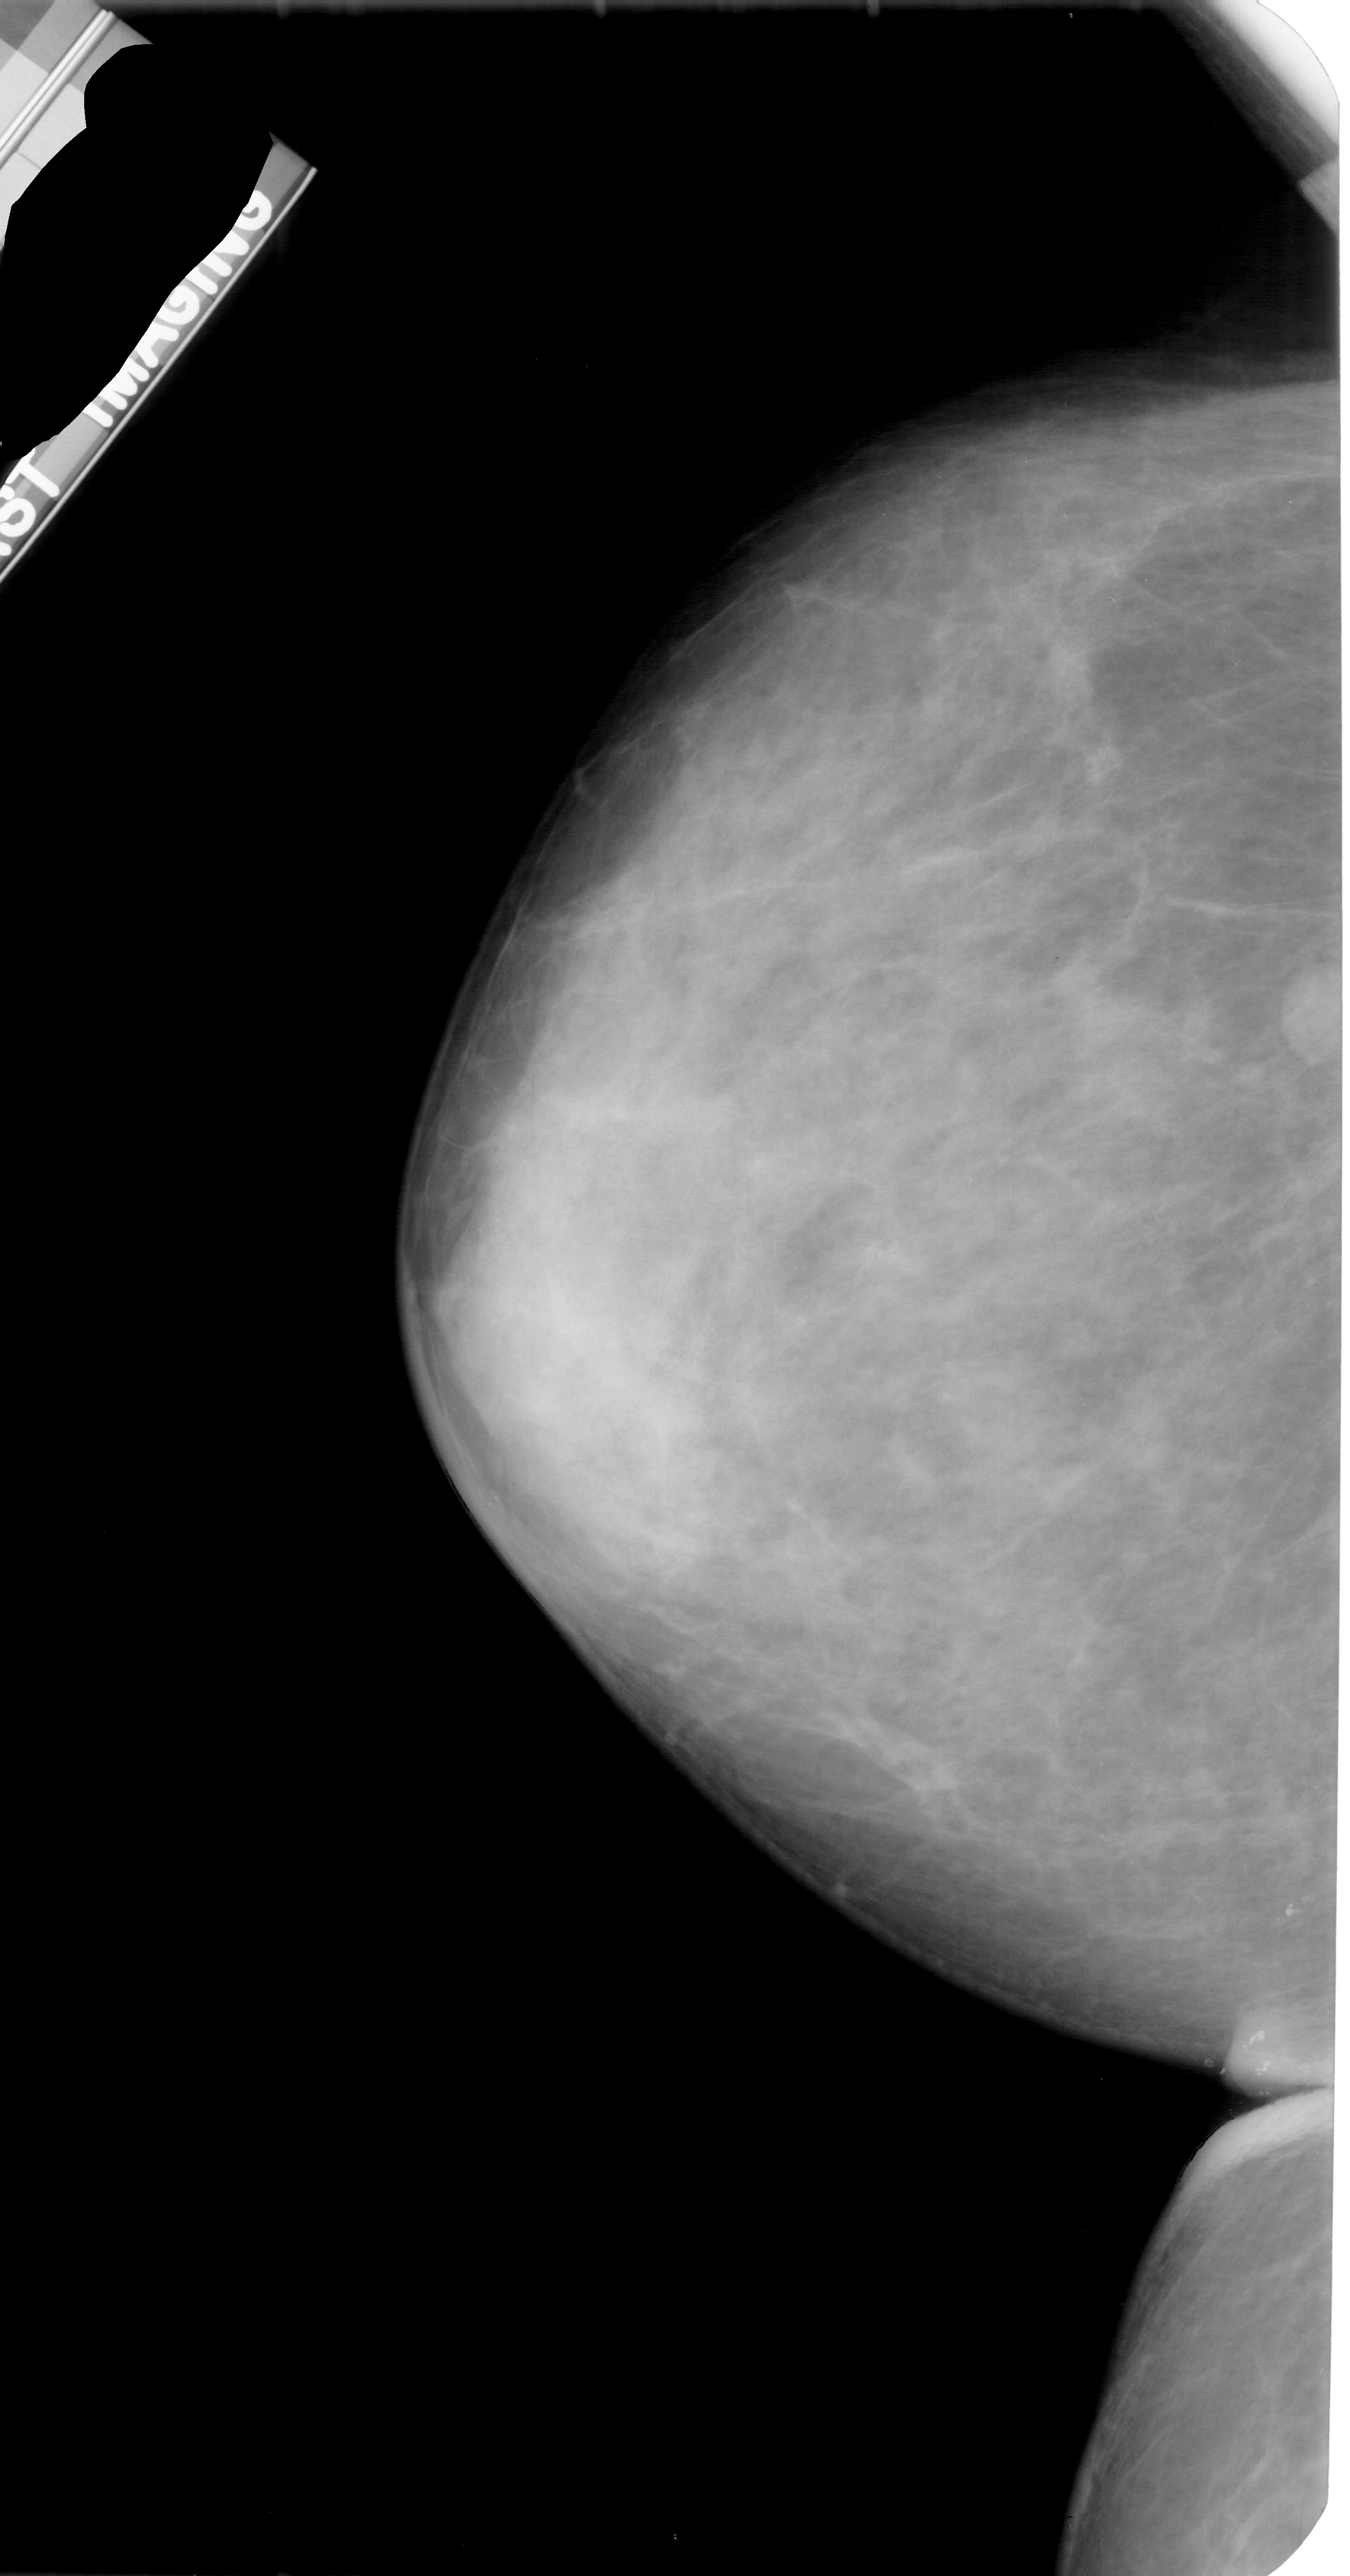
Scanned film-screen mammogram; left breast; craniocaudal (CC) view; BI-RADS breast density category 3 (scale 1–4).
Marked abnormality: mass, shape round, margins circumscribed; BI-RADS assessment category 3; subtlety rating 4 on a 1 (subtle) to 5 (obvious) scale; pathology result (as recorded, not read from the image): benign.